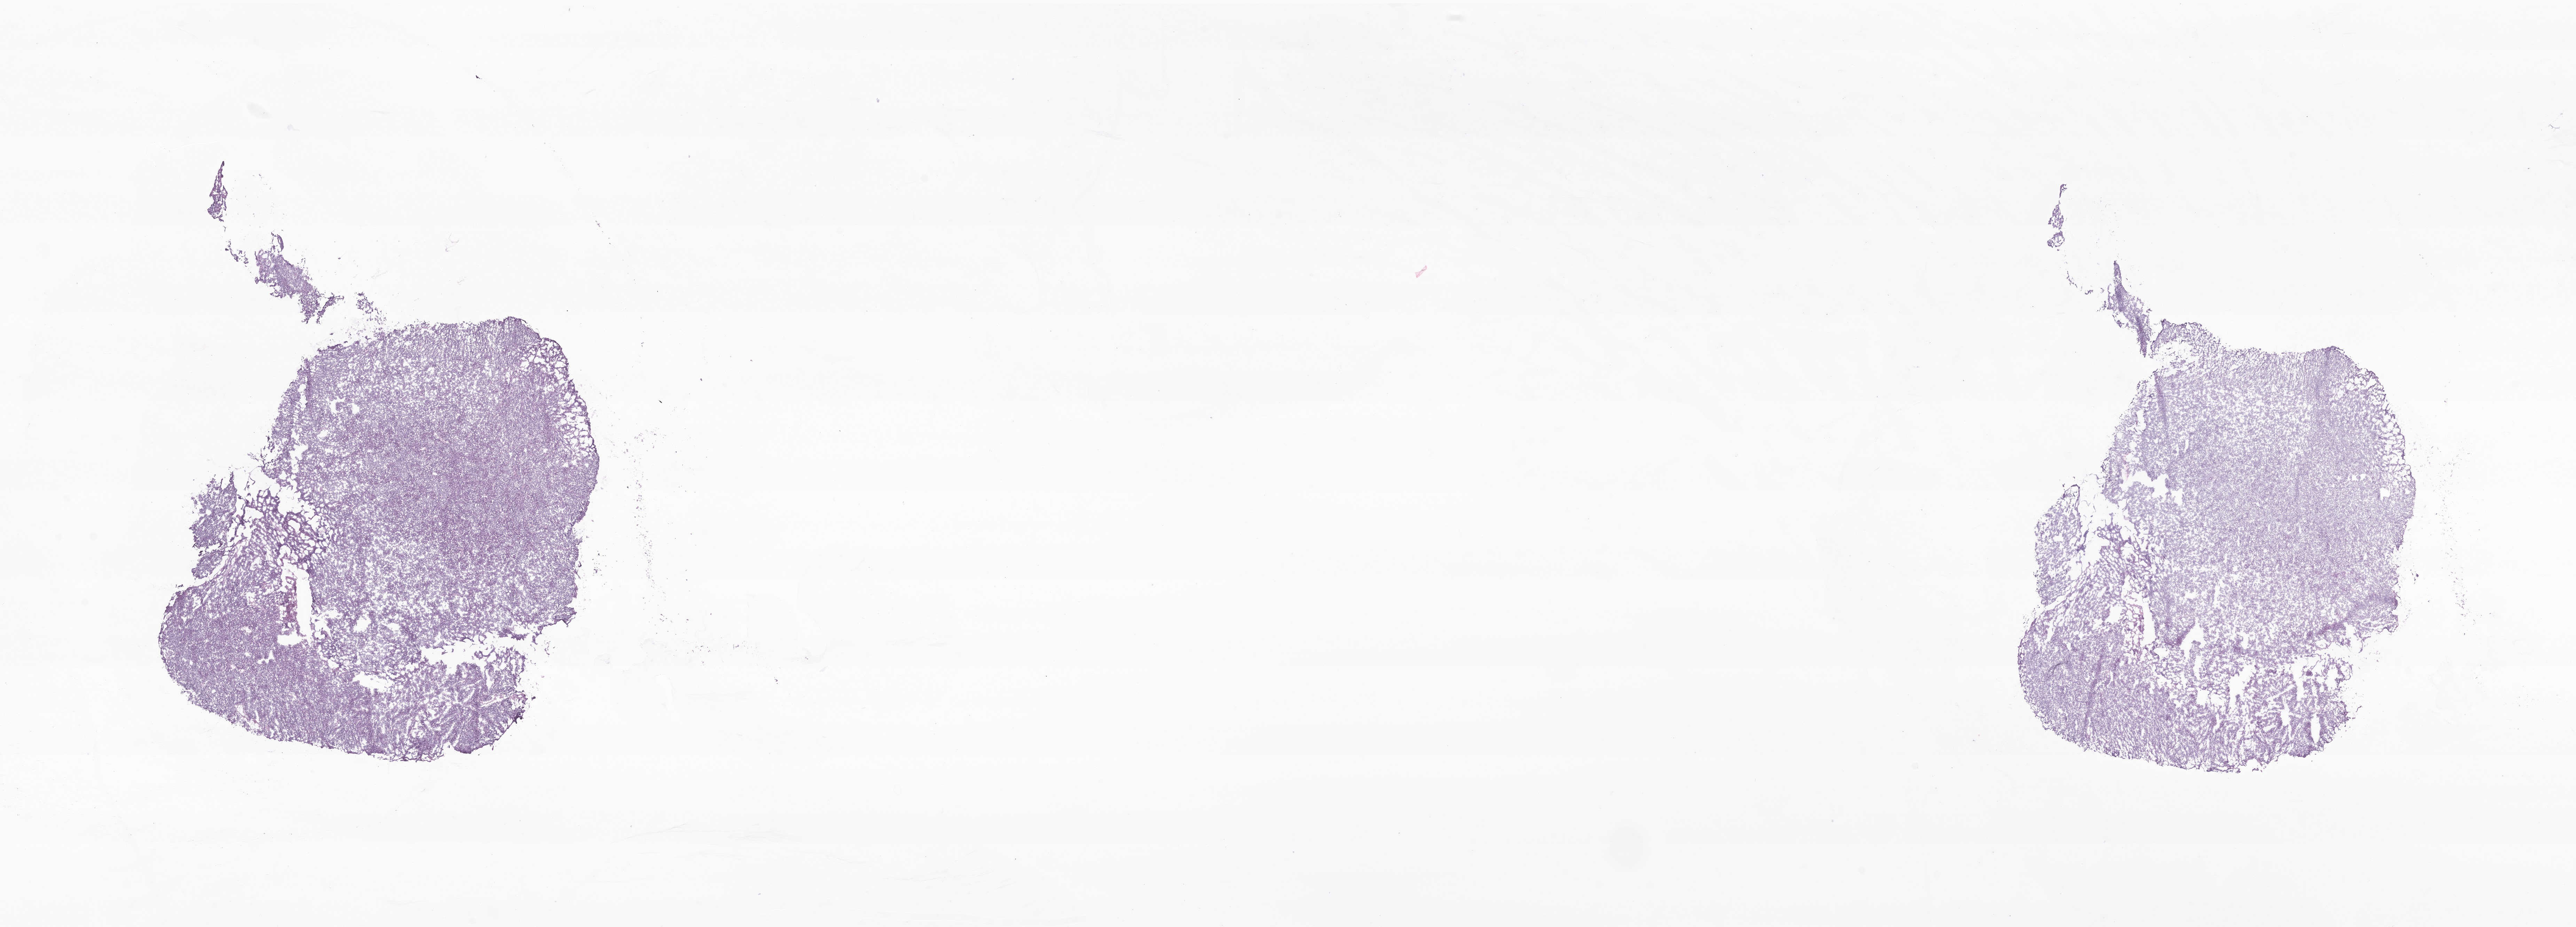
Whole-slide image, haematoxylin and eosin stain of tumor tissue from the brain, low-resolution overview of the scanned area, about 31.1 x 11.2 mm, frozen section (OCT-embedded). Patient male; age 224 months (18 years 8 months).
Diagnosis: Neoplasm, malignant.